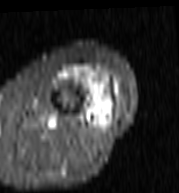
MRI of an extremity soft-tissue mass, one axial slice. Position 34 of 103 along the scan axis. STIR. MR volume resampled by the dataset authors to the PET/CT grid (not the native acquisition matrix). 179 × 193 image matrix, field of view 175 × 188 mm. Female patient. Case-level facts recorded for this patient, not image findings: histological type: undifferentiated – high grade; grade: high; site of the primary tumour: left thigh.
Structures marked on this image (expert contour drawn on MRI and transferred to this co-registered scan by the dataset authors):
- gross tumour volume including surrounding oedema: bounding box <61,66,119,122> (left, top, right, bottom; pixels)